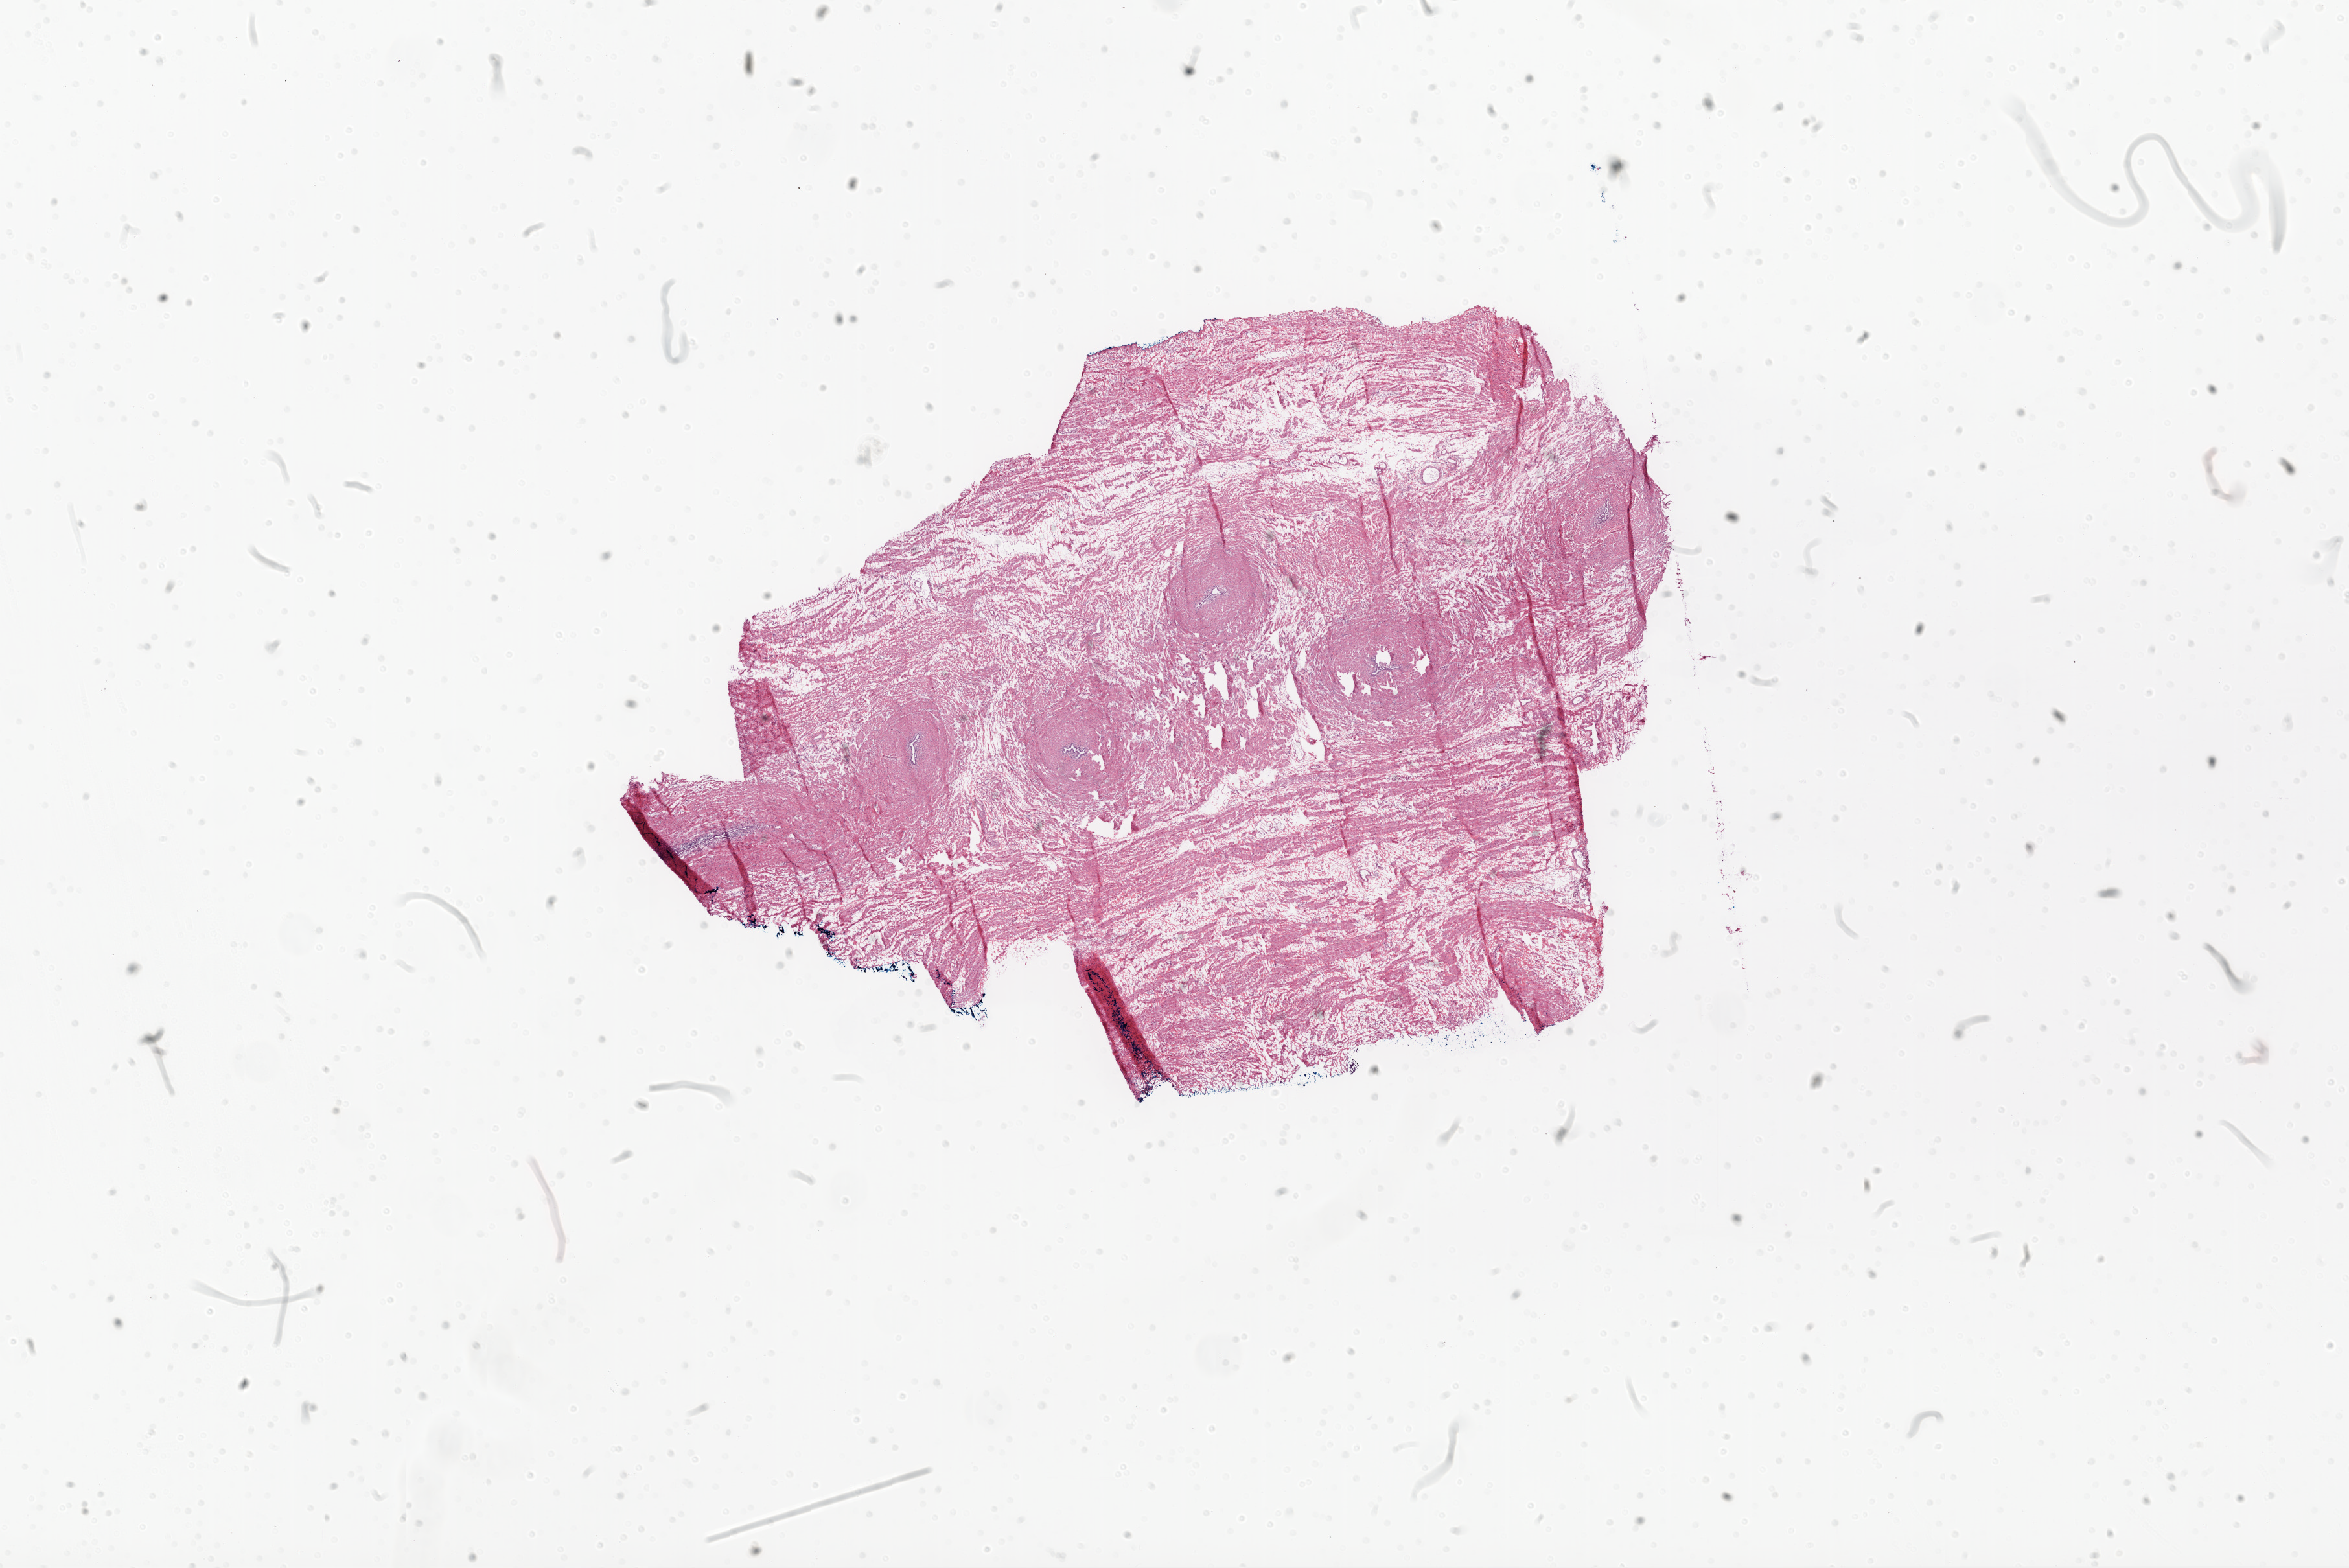
Hematoxylin and eosin (H&E) stained whole-slide image, whole scanned area (about 29.1 x 19.4 mm, from a 20x scan) shown as a low-resolution overview; frozen section; ovary, solid tissue normal (non-tumour tissue) sample. Patient: female, age at initial diagnosis 56 years.
This section: solid tissue normal sample (biorepository sample class). Patient diagnosis: Serous cystadenocarcinoma, NOS.